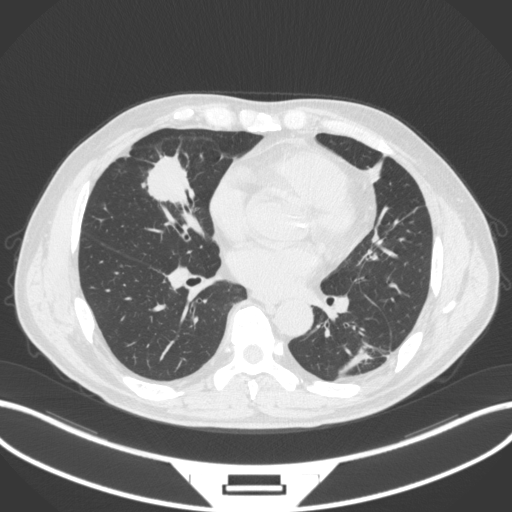
Chest CT, one axial slice. Position 130 of 399 along the scan axis. 120 kVp. Lung window (W 1500 / L -600 HU). 1 mm slice thickness. 512 × 512 image matrix, field of view 400 × 400 mm. Patient: male, 59 years. From the clinical record (not read from this slice): clinical TNM (as recorded): T2a N1 M0.
Outlined on this slice (rectangle marked by the reading radiologist):
- lung tumour (recorded histology: adenocarcinoma): bounding box [x1, y1, x2, y2] px = [138, 151, 199, 211]